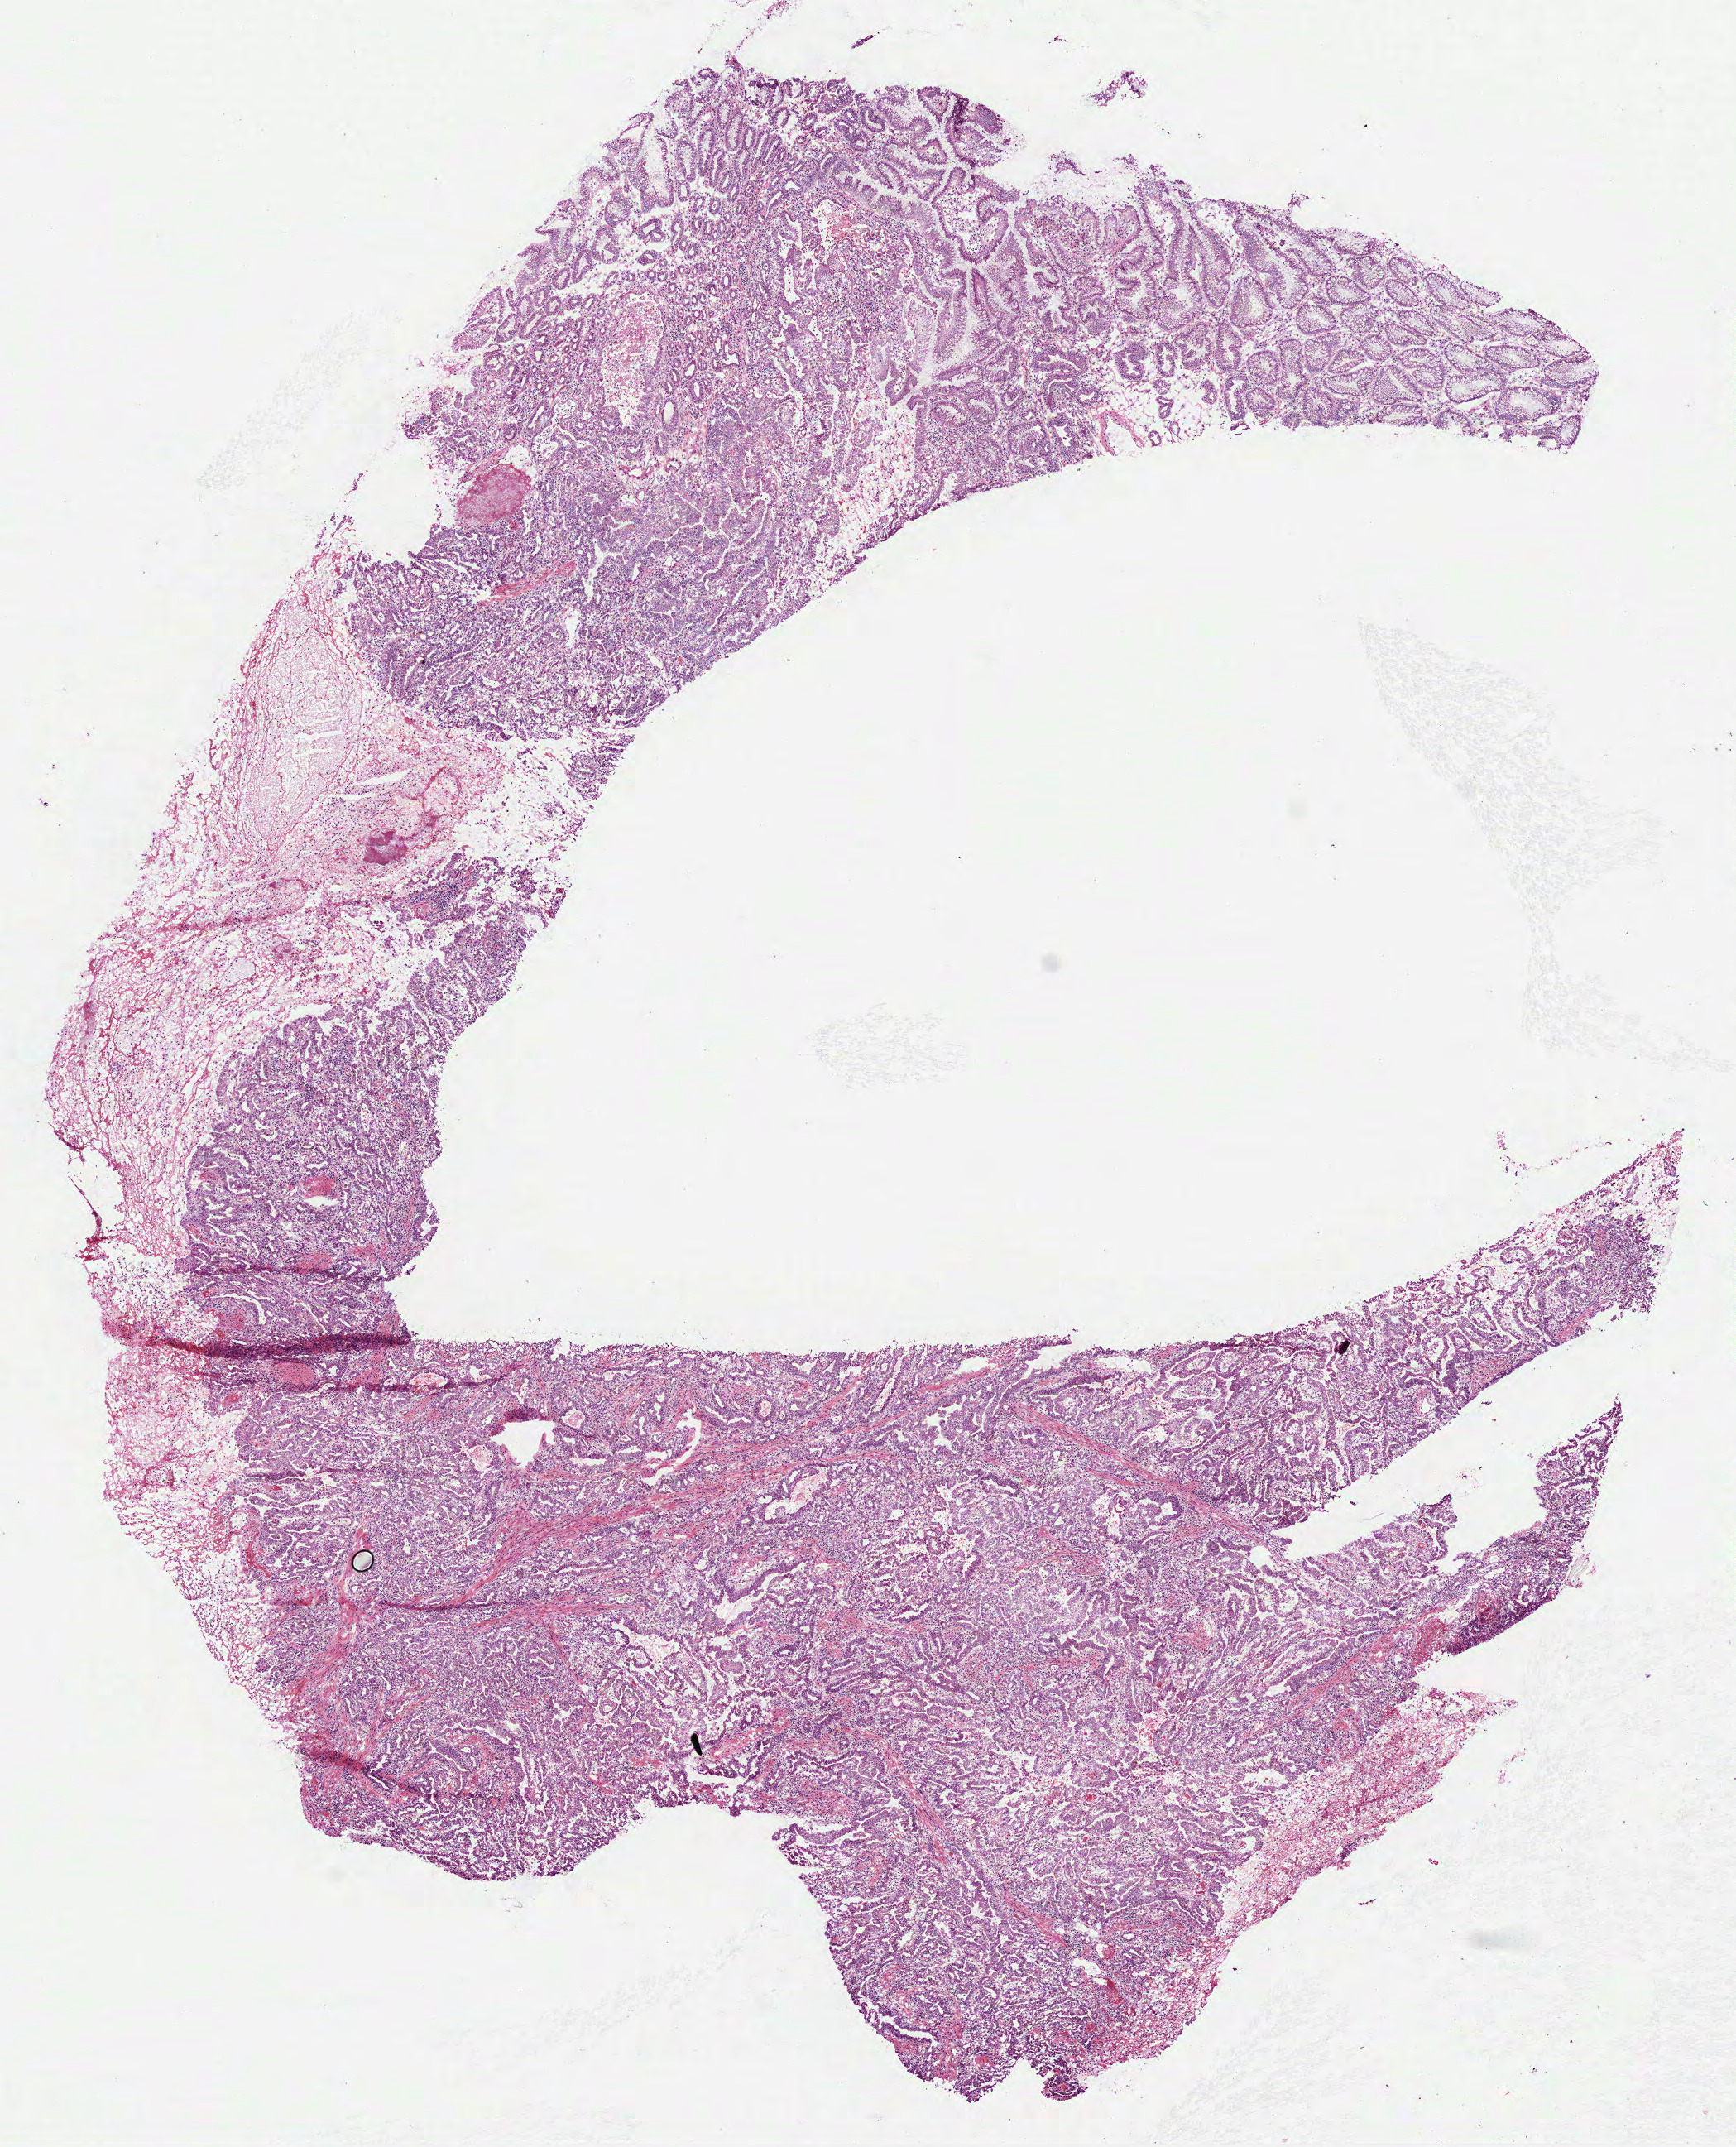
Digitized Hematoxylin and eosin (H&E) stained tissue section (whole slide) — low-resolution overview of the scanned area, about 8.5 x 10.5 mm (slide scanned at 40x), frozen section from the bottom of the tissue portion, primary tumour sample from the stomach. Patient sex: female.
Histologic diagnosis: Adenocarcinoma, NOS.